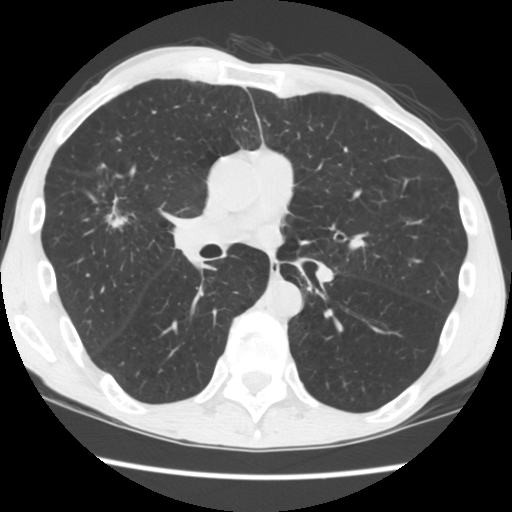
Low-dose screening chest CT, one axial slice. Slice 94 of 181 in the series (ordered by position). 120 kVp. Lung window (W 1500 / L -600 HU). 2.5 mm slice thickness. 512 × 512 image matrix.
Annotated regions visible in this slice (outlined manually by an expert reader):
- lesion 1 (tumor, upper lobe of right lung): bounding box <106,196,128,228> (left, top, right, bottom; pixels)